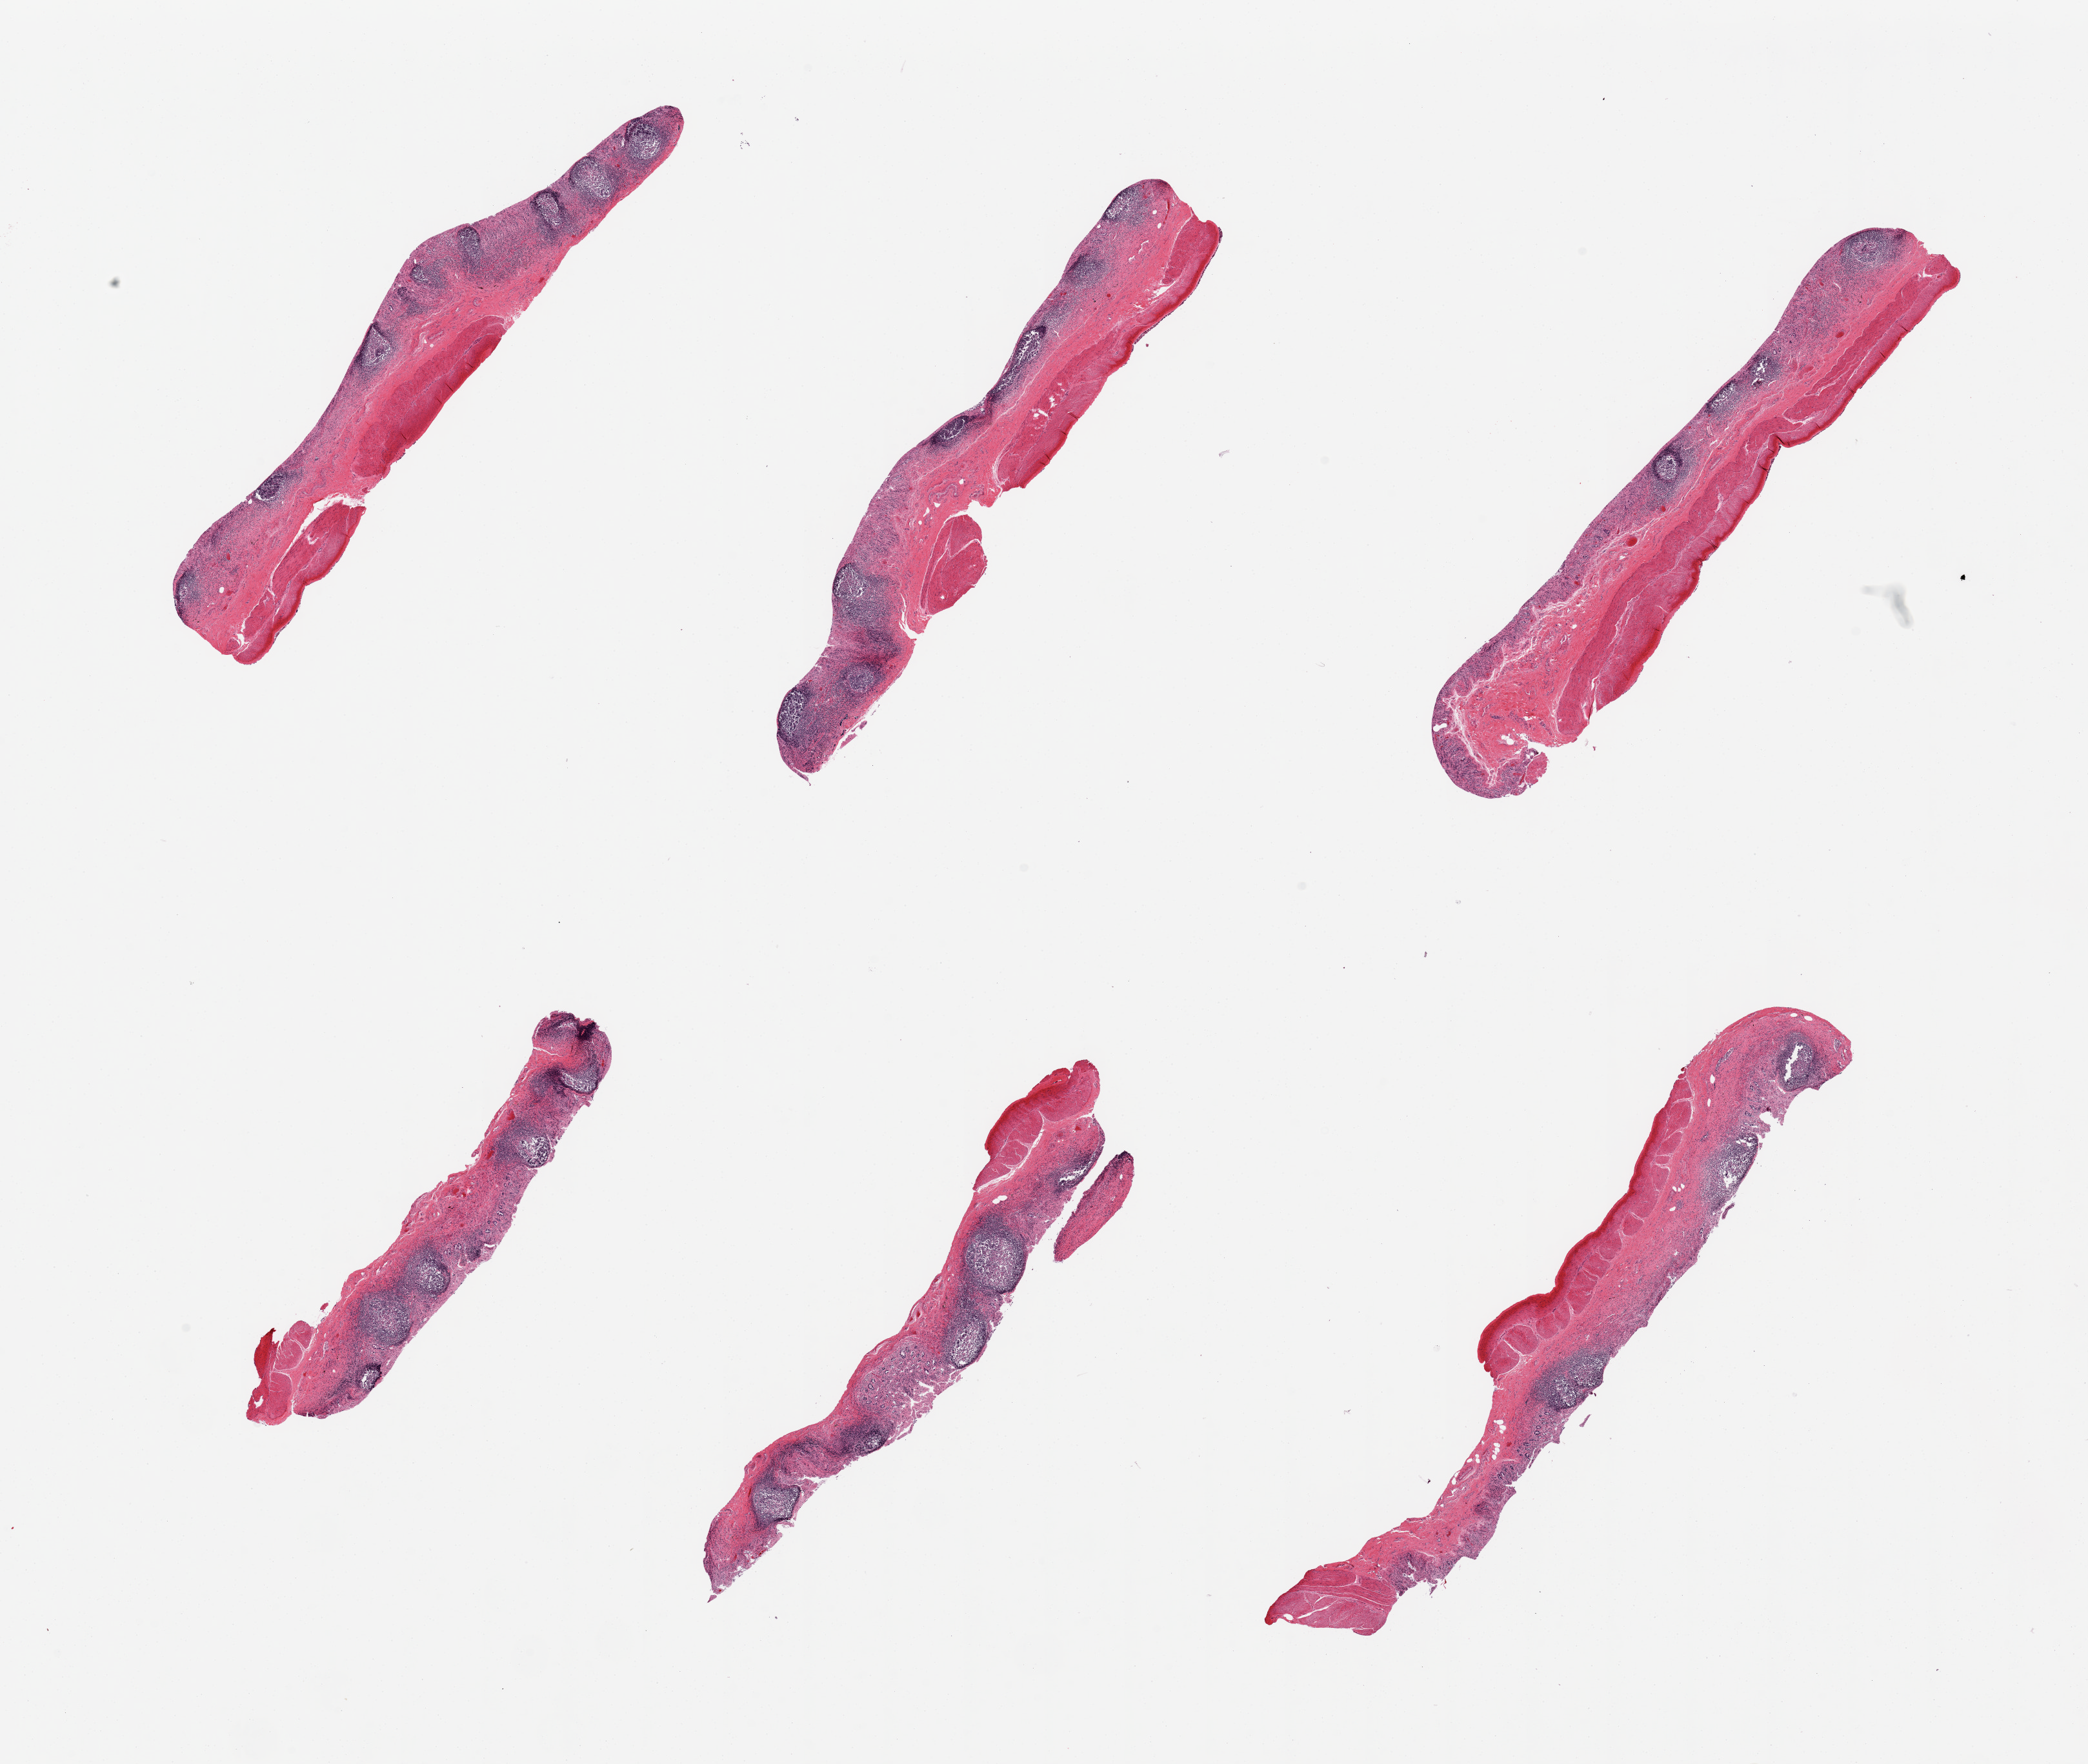
H&E whole-slide image, brightfield — whole scanned area (about 25.6 x 21.6 mm, from a 20x scan) shown as a low-resolution overview, PAXgene-fixed paraffin-embedded (PFPE) section, sampled site (target tissue): ileum, donor tissue sample.
Reviewer comment on this tissue sample: 6 pieces, severely autolyzed mucosa, muscularis present in several sections (not target), good representation of lymphoid tissue.